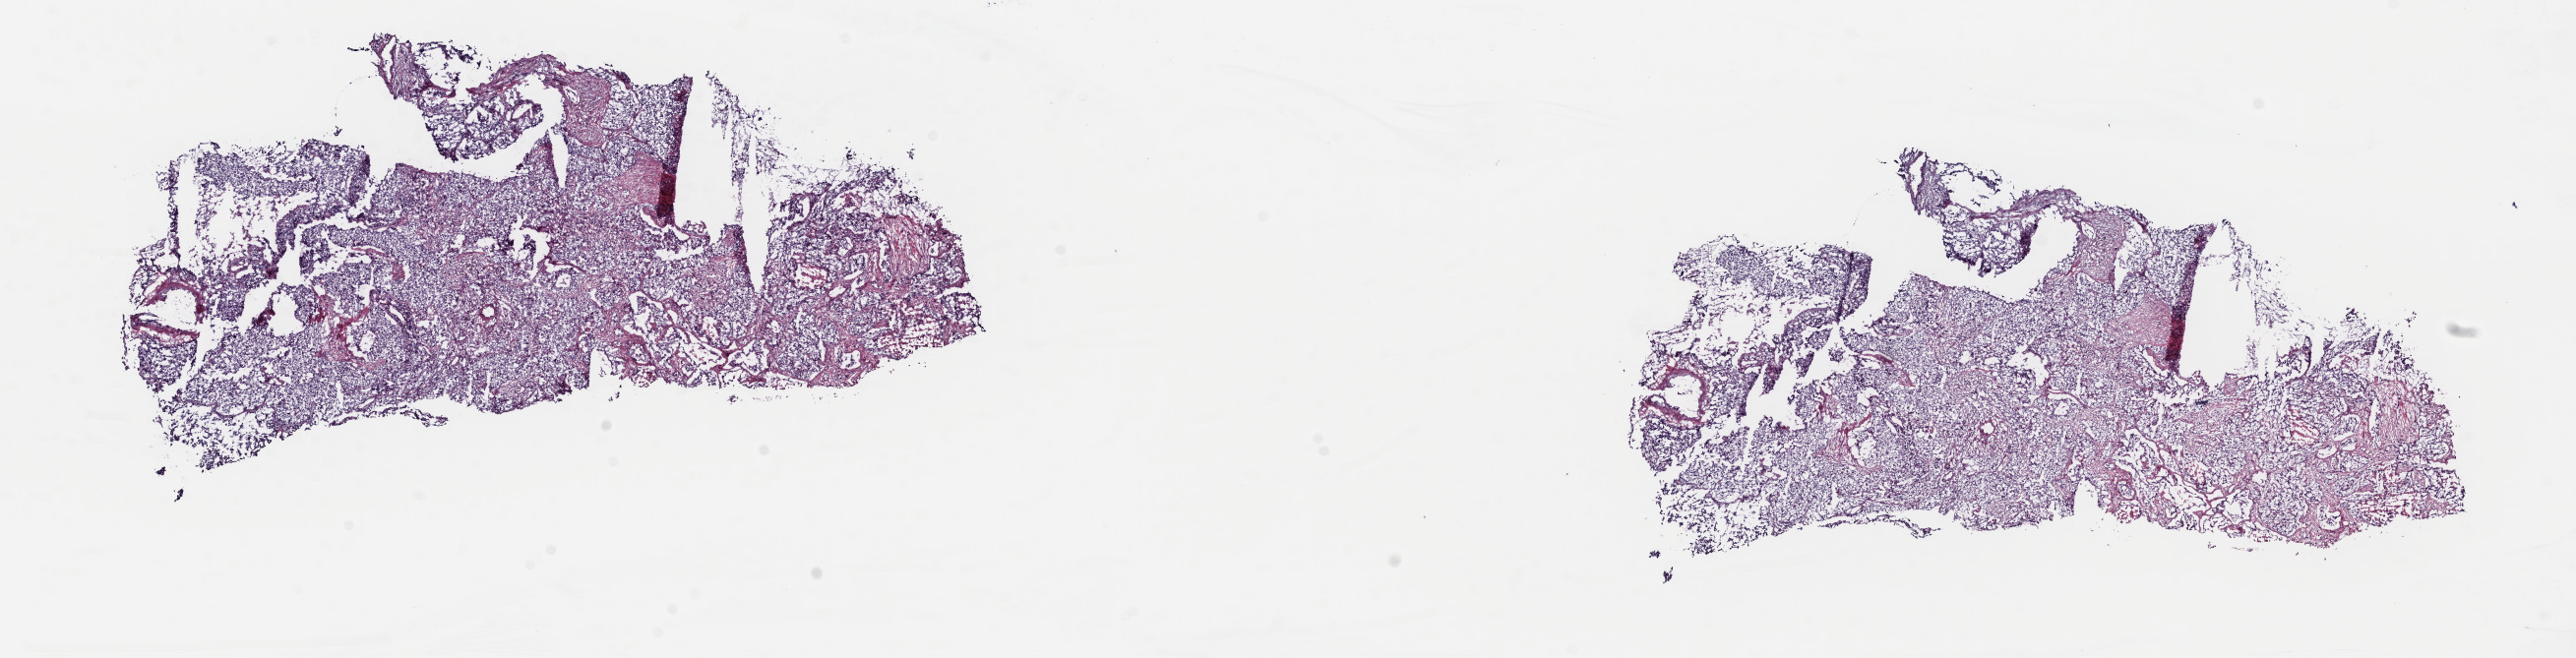
Whole-slide histology image, H&E — whole scanned area (about 20.7 x 5.3 mm, acquisition: 40x scan) shown as a low-resolution overview; frozen section from the top of the tissue portion; primary tumour sample from the lung. Female, age 58 years at initial diagnosis. Slide review estimates, as recorded: tumour cells 75%, tumour nuclei 100%, normal cells 0%, stromal cells 20%, necrosis 5%. Infiltration values recorded for this section: lymphocyte infiltration 2%, monocyte infiltration 1%, neutrophil infiltration 0%.
Diagnosis: Squamous cell carcinoma, NOS. AJCC pathologic stage: IIB.